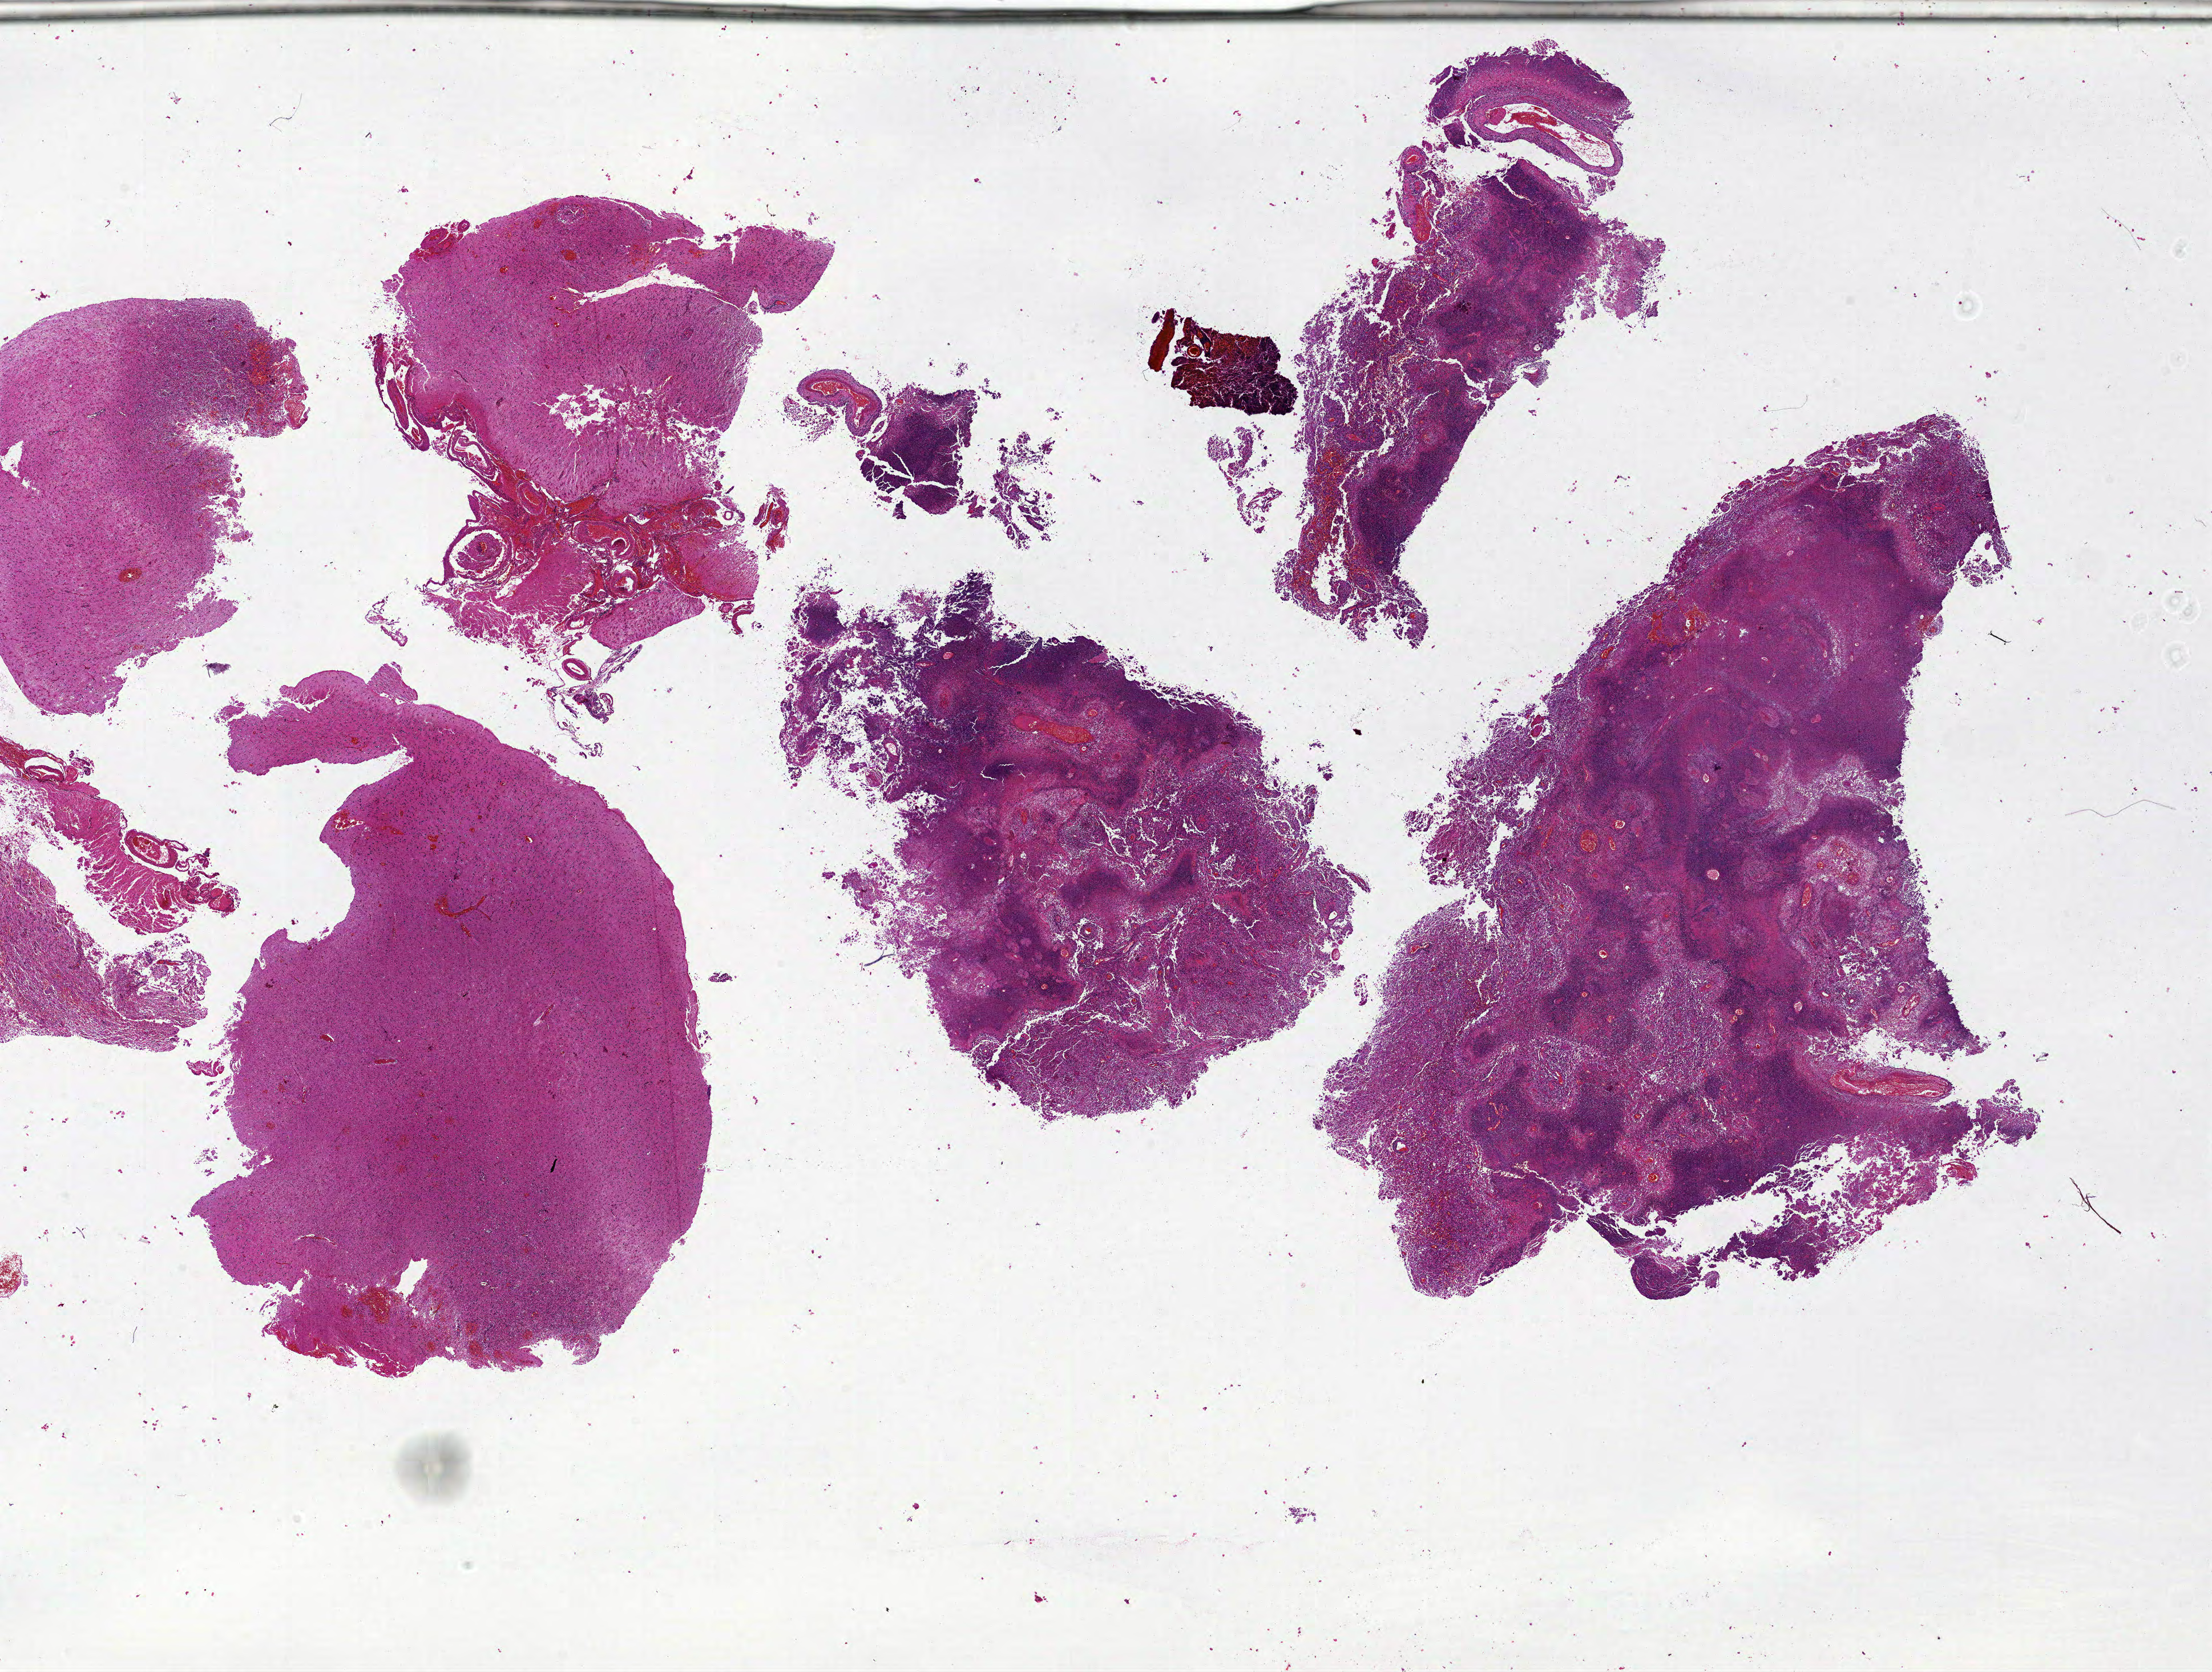
Digitized Hematoxylin and eosin (H&E) stained tissue section (whole slide), whole scanned area (about 31.0 x 23.4 mm) shown as a low-resolution overview; FFPE section; brain, primary tumour sample. Patient: male, age at initial diagnosis 46 years.
Histologic diagnosis: Glioblastoma.